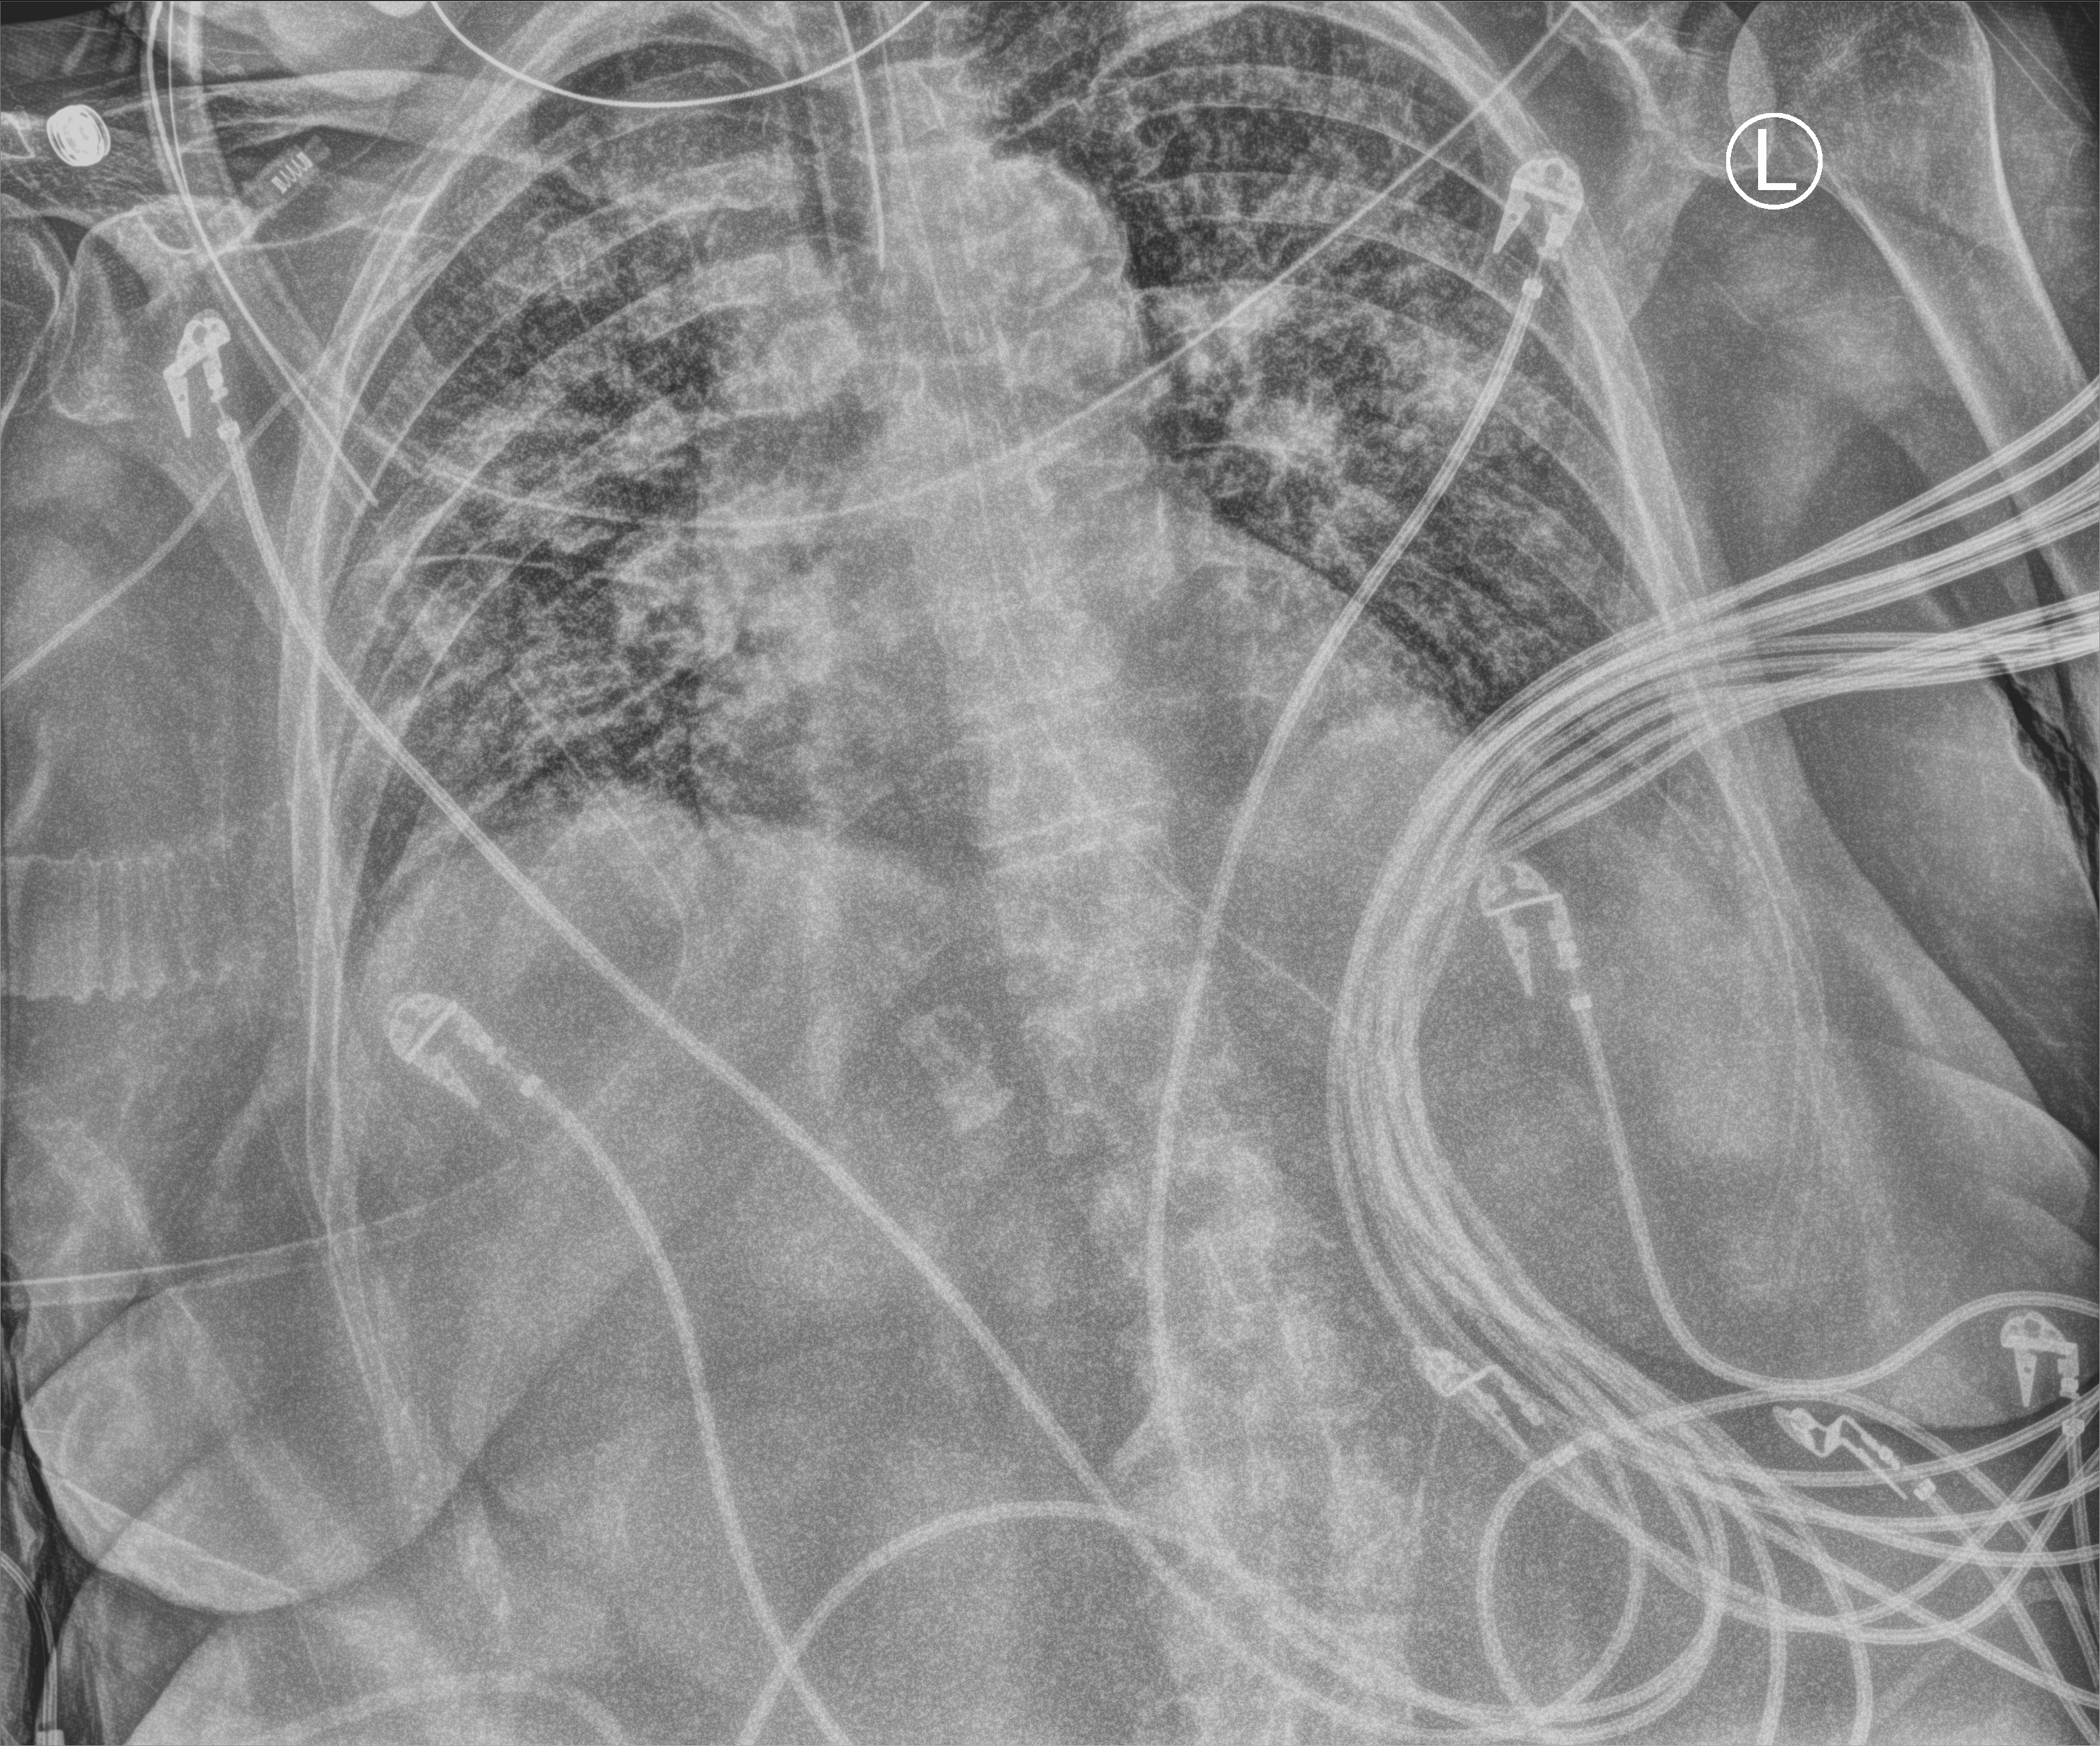
Bedside chest radiograph (computed radiography), anteroposterior (AP) projection. Female patient hospitalised with COVID-19, age 75–90 years.
Admission-level facts for this patient (not findings on this image; timing relative to this image not recorded): admitted to intensive care during this hospital stay: yes; mechanically ventilated during this hospital stay: yes.